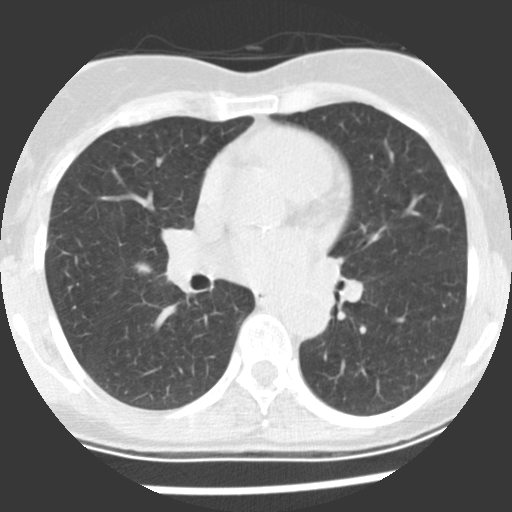
Low-dose screening chest CT, one axial slice. Slice 116 of 225 in the series (ordered by position). 120 kVp. Lung window (W 1500 / L -600 HU). 512 × 512 image matrix, field of view 270 × 270 mm.
Structures marked on this image (outlined manually by an expert reader):
- lesion 1 (tumor, upper lobe of right lung): bounding box [x1, y1, x2, y2] px = [136, 263, 150, 273]